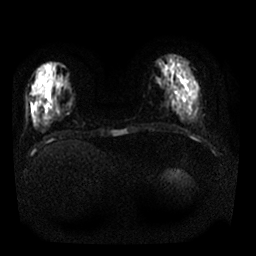
Breast MRI, one axial slice. Position 8 of 25 along the scan axis. Diffusion-weighted series; image 2 of 4 stored at this slice position (different b-values; order by instance number). 1.5 T. 256 × 256 image matrix, field of view 330 × 330 mm. Female patient.
Structures marked on this image (expert manual segmentation):
- tumour on diffusion-weighted imaging: box from (x=180, y=97) to (x=192, y=109) px